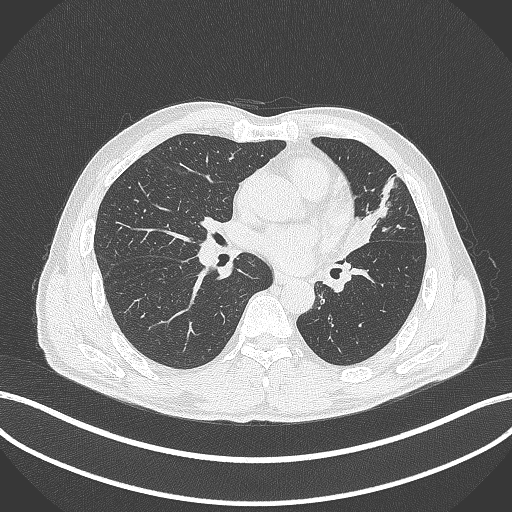
Chest CT, one axial slice. Position 214 of 429 along the scan axis. Lung window (W 1500 / L -600 HU). 1 mm slice thickness. 512 × 512 image matrix, field of view 400 × 400 mm. Patient: male, 57 years. Case-level facts recorded for this patient, not image findings: clinical TNM (as recorded): T2b N0 M0.
Annotated regions visible in this slice (bounding box drawn by a radiologist):
- lung tumour (recorded histology: squamous cell carcinoma): bounding box (x1, y1, x2, y2) in pixels: (345, 209, 379, 255)